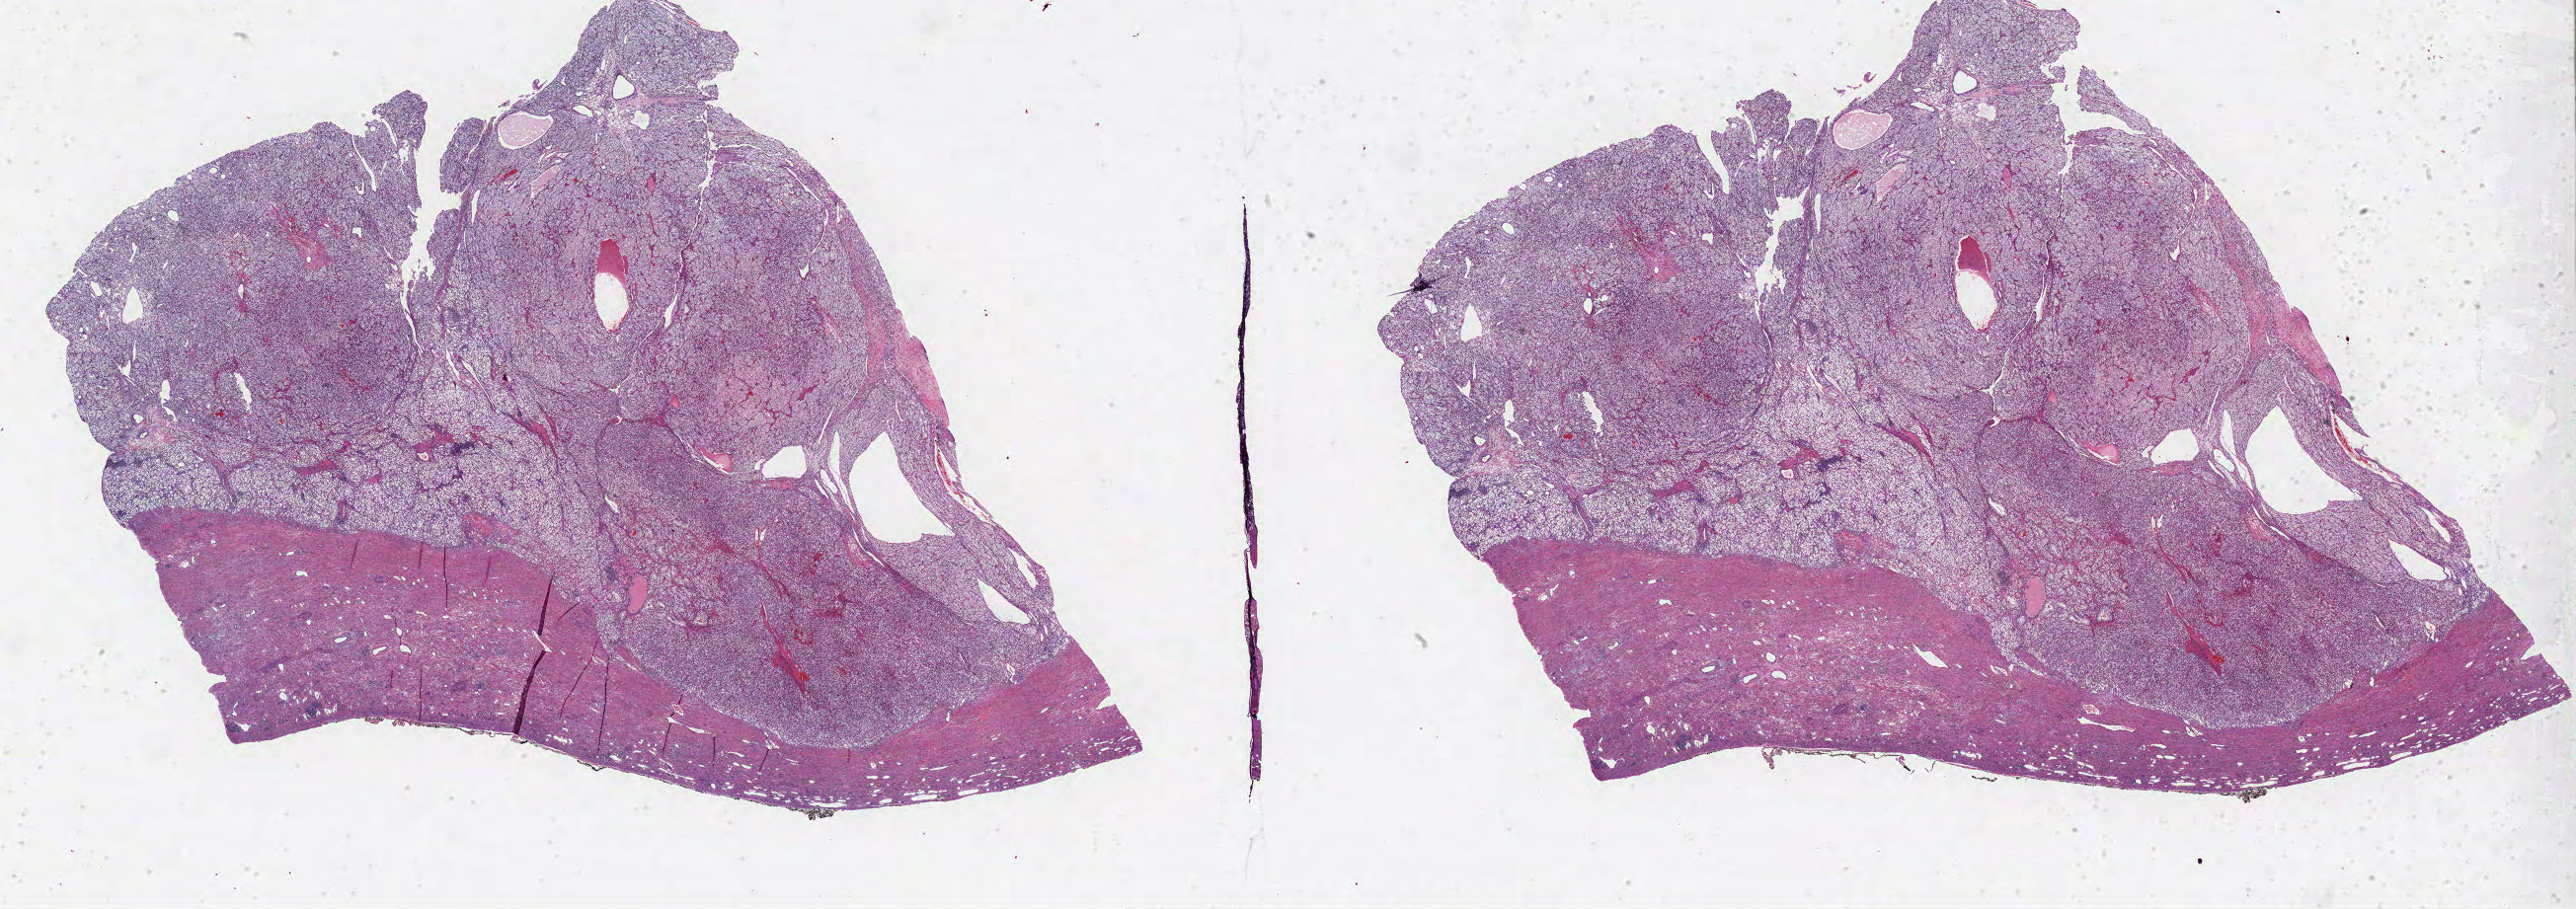
H&E-stained whole-slide image, shown as a low-resolution overview of the whole scanned area (about 41.7 x 14.7 mm, slide scanned at 40x), formalin-fixed paraffin-embedded (FFPE) diagnostic section, sample: primary tumour, kidney. Patient: male, age at initial diagnosis 45 years. Histologic grade: G2 (moderately differentiated).
AJCC pathologic stage: II. Histologic diagnosis: Clear cell adenocarcinoma, NOS. Lymph nodes positive (case pathology): 0 of 10 examined. Laterality: left.